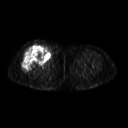
FDG PET of an extremity soft-tissue mass (from a PET/CT study), one axial slice. Position 256 of 311 along the scan axis. 3.27 mm slice thickness. 128 × 128 image matrix, field of view 500 × 500 mm. Patient: female, 57 years. Case-level facts recorded for this patient, not image findings: histological type: pleiomorphic undifferentiated sarcoma; grade: high; site of the primary tumour: right quadricep.
Annotated regions visible in this slice (expert contour drawn on MRI and transferred to this co-registered scan by the dataset authors):
- tumour plus oedema (research contour): box from (x=22, y=45) to (x=50, y=72) px
- tumour (research contour): (x=22, y=45)–(x=50, y=72)